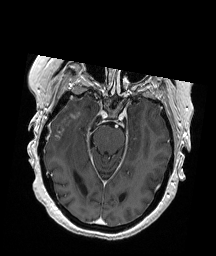
Brain MRI from a brain-tumour surgery series, one axial slice. Position 128 of 192 along the scan axis. T1-weighted post-contrast. 216 × 256 image matrix. Case-level facts recorded for this patient, not image findings: histopathology: Glioblastoma; WHO grade: 4; IDH mutation: no; tumour location: Right Temporal.
Structures marked on this image (expert manual segmentation):
- tumour: bounding box (x1, y1, x2, y2) in pixels: (54, 113, 79, 140)